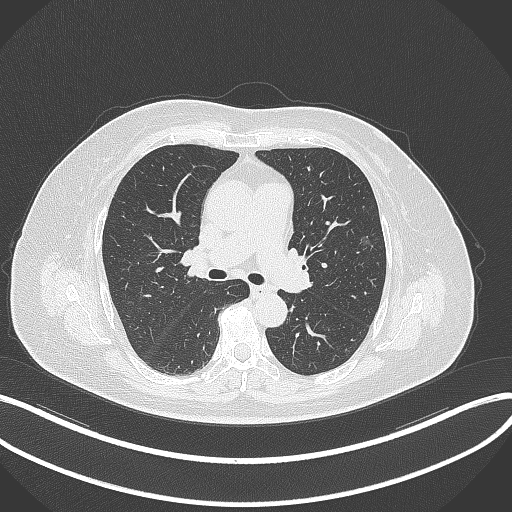
Chest CT, one axial slice. Slice 218 of 315 in the series (ordered by position). Reconstruction kernel B70f. 120 kVp. Lung window (W 1500 / L -600 HU). 1 mm slice thickness. 512 × 512 image matrix. Female patient, age 76 years. Case-level facts recorded for this patient, not image findings: clinical TNM (as recorded): T1b N0 M0.
Annotated regions visible in this slice (bounding box drawn by a radiologist):
- lung tumour (recorded histology: adenocarcinoma): bounding box (x1, y1, x2, y2) in pixels: (357, 229, 380, 257)